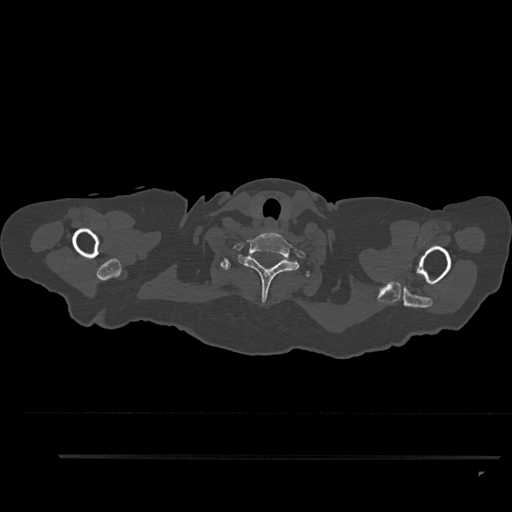
CT including the spine, one axial slice. Slice 789 of 797 in the series (ordered by position). Bone window (W 1800 / L 400 HU). 512 × 512 image matrix, field of view 408 × 408 mm. Female patient, age 44 years. From the clinical record (not read from this slice): primary cancer: renal; vertebrae with lytic lesions (as recorded): L1.
Annotated regions visible in this slice (semi-automatic segmentation, software-assisted and operator-edited):
- T1 vertebra: bounding box (x1, y1, x2, y2) in pixels: (221, 258, 309, 277)